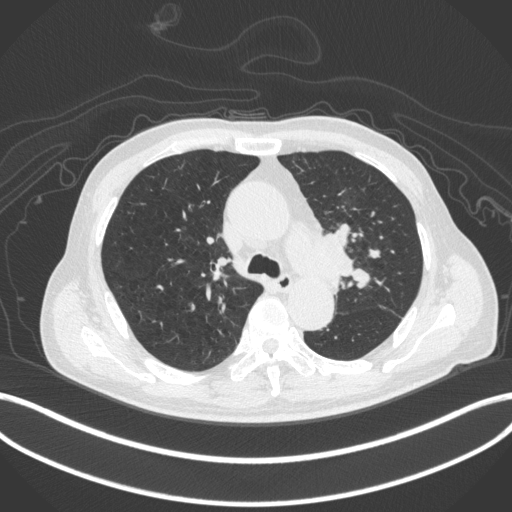
Chest CT, one axial slice. Slice 293 of 420 in the series (ordered by position). 120 kVp. Lung window (W 1500 / L -600 HU). 512 × 512 image matrix, field of view 400 × 400 mm. Patient: male, 77 years. Case-level facts recorded for this patient, not image findings: clinical TNM (as recorded): T3 N1 M0.
Annotated regions visible in this slice (rectangle marked by the reading radiologist):
- lung tumour (recorded histology: adenocarcinoma): bounding box [x1, y1, x2, y2] px = [304, 228, 357, 282]